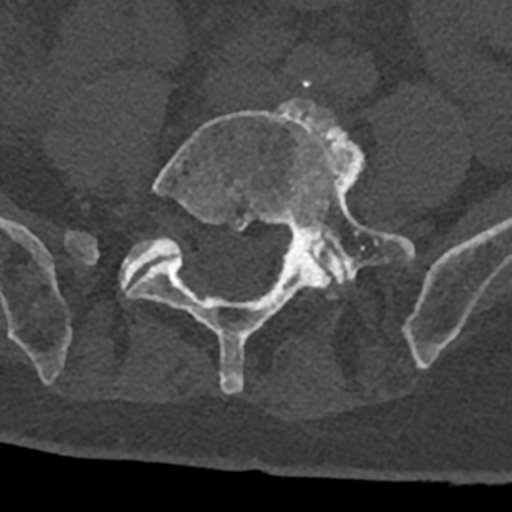
CT including the spine, one axial slice; slice 198 of 797 in the series (ordered by position); reconstruction kernel Br40s/3; 120 kVp; bone window (W 1800 / L 400 HU); 0.5 mm slice thickness; 512 × 512 image matrix, field of view 160 × 160 mm. Male patient, age 74 years. Case-level facts recorded for this patient, not image findings: primary cancer: renal; vertebrae with lytic lesions (as recorded): T10, L1, L2, L3, L4, L5.
Outlined on this slice (semi-automatically segmented with operator editing):
- L4 vertebra: bounding box [x1, y1, x2, y2] px = [301, 286, 311, 290]
- L5 vertebra: [127, 99, 415, 394]